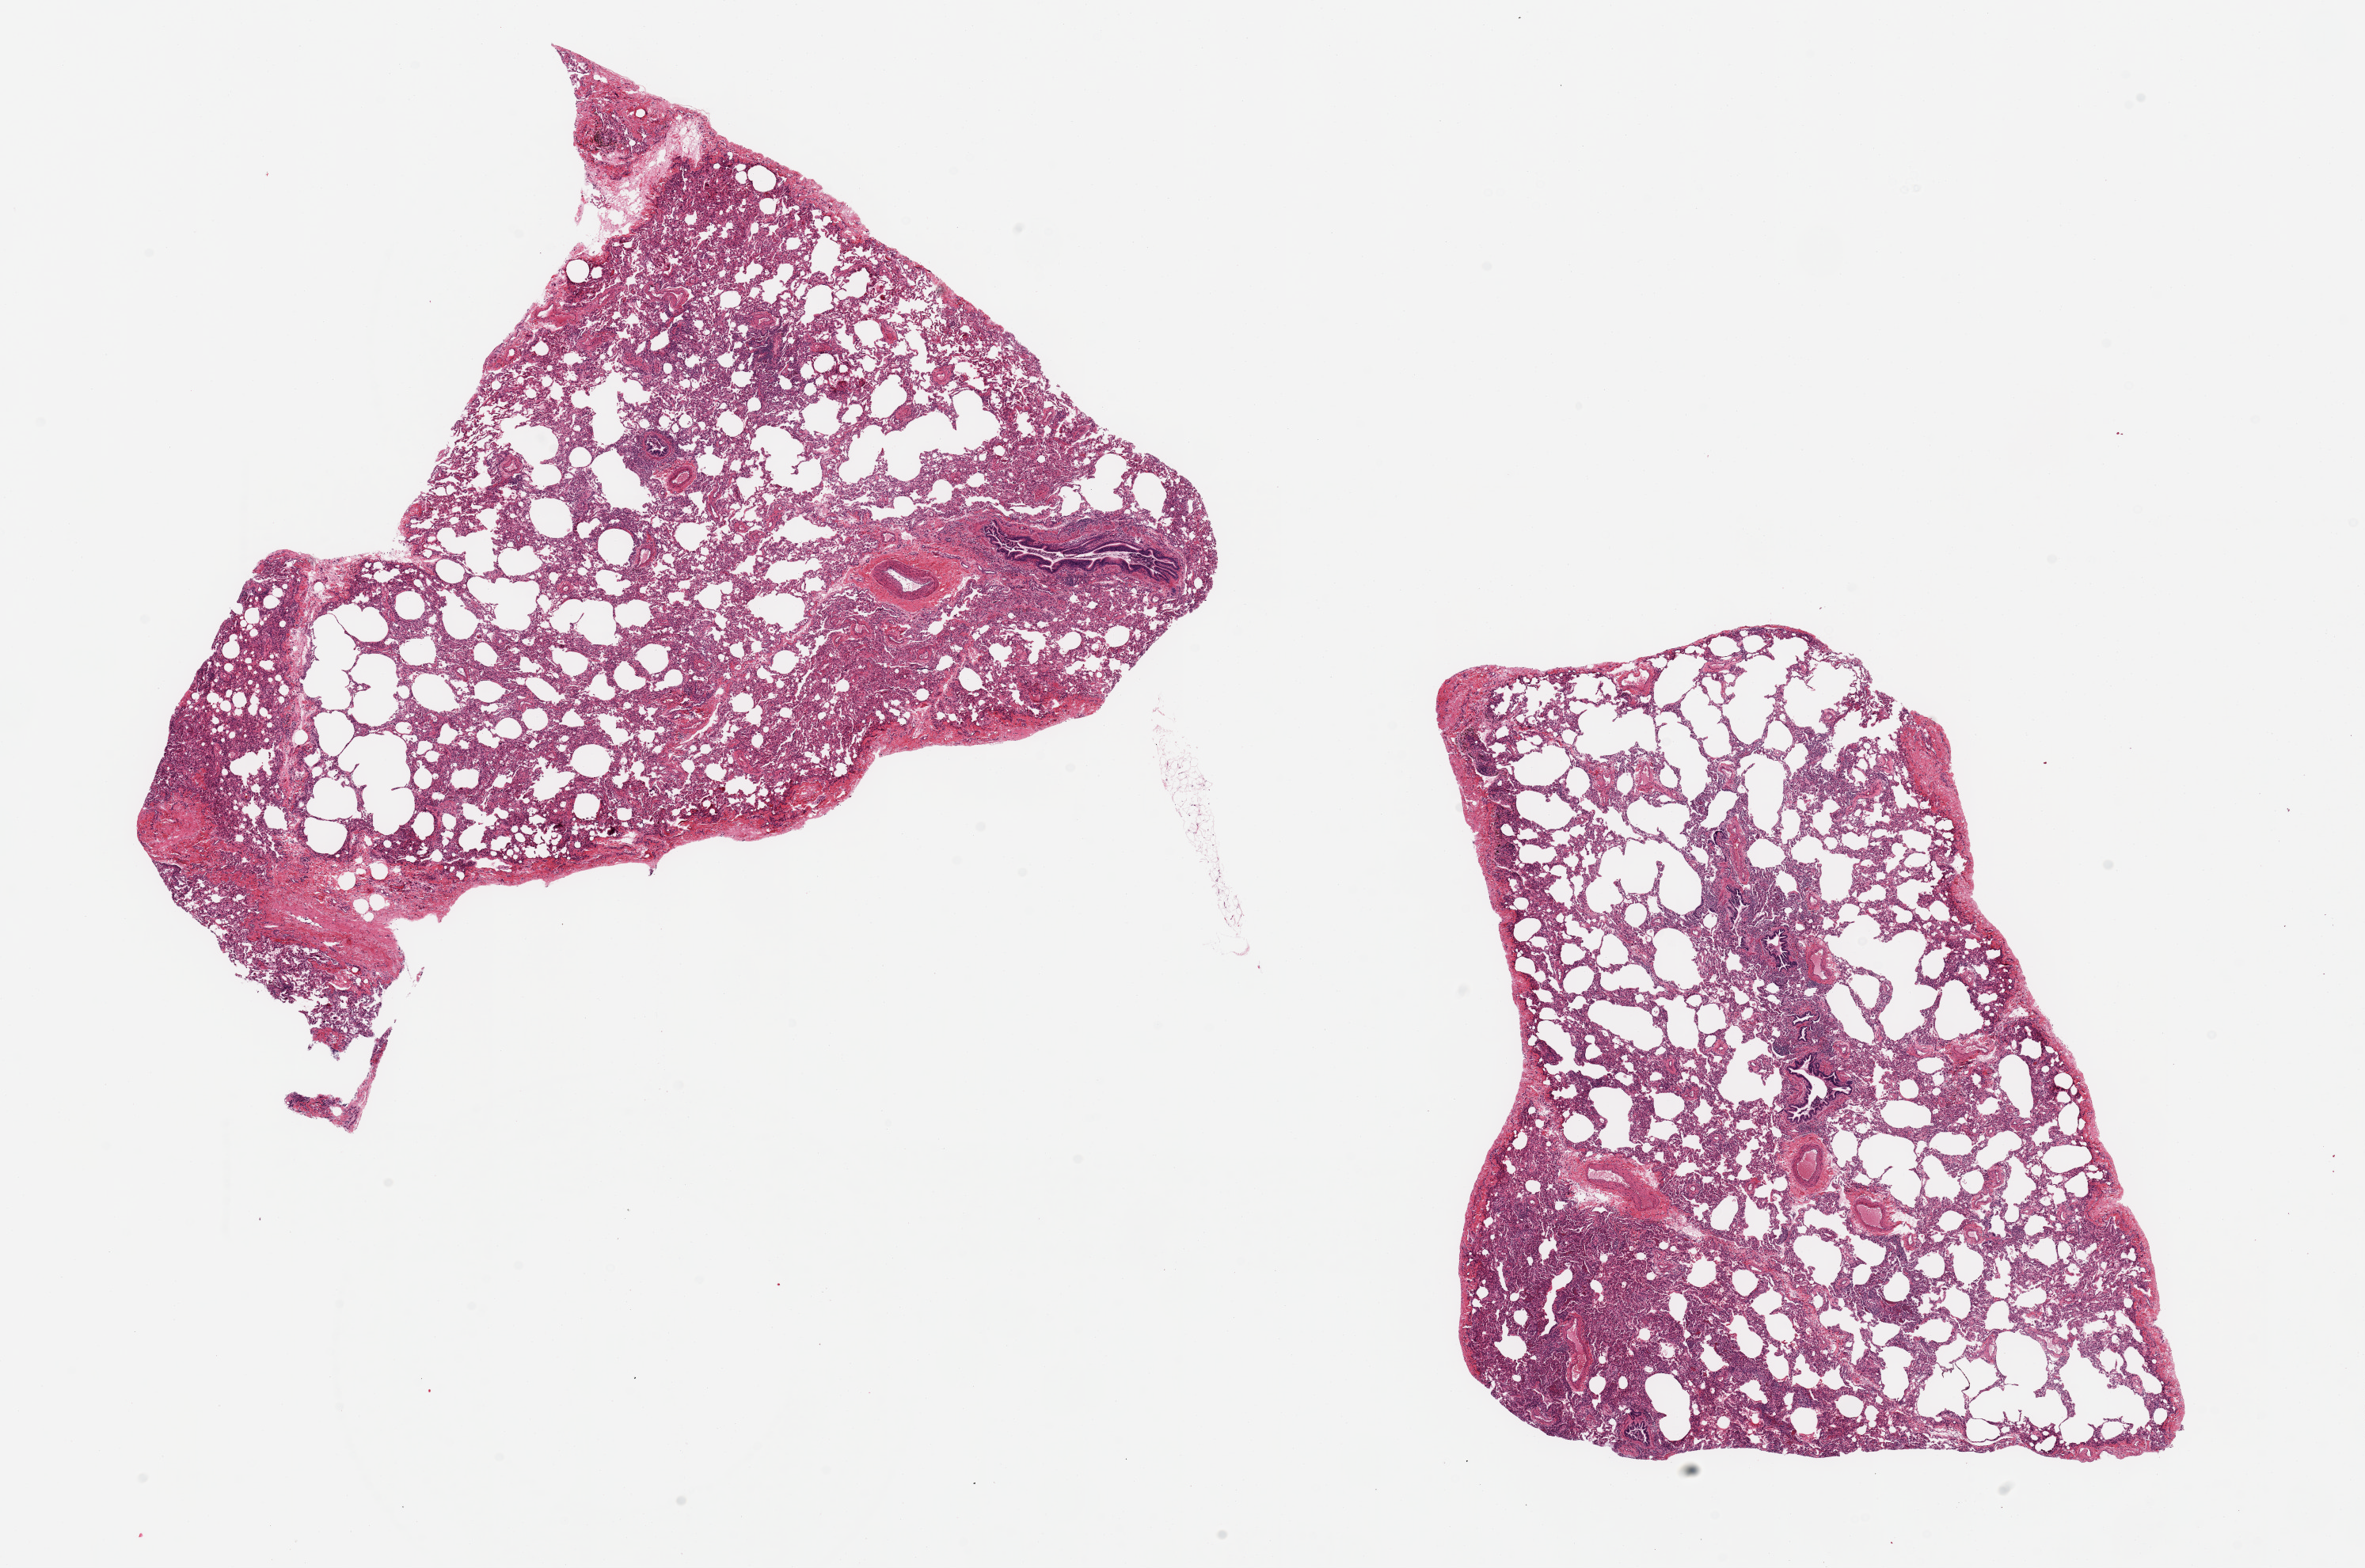
Digitized hematoxylin and eosin (H&E)-stained section, brightfield, whole scanned area (about 23.6 x 15.7 mm) shown as a low-resolution overview; PAXgene-fixed paraffin-embedded (PFPE) section; section of lung (target tissue); donor tissue sample. Donor sex: male.
Review note (as recorded): 2 ~10x7 & 8x7mm pieces. Patchy bronchopneumonia.